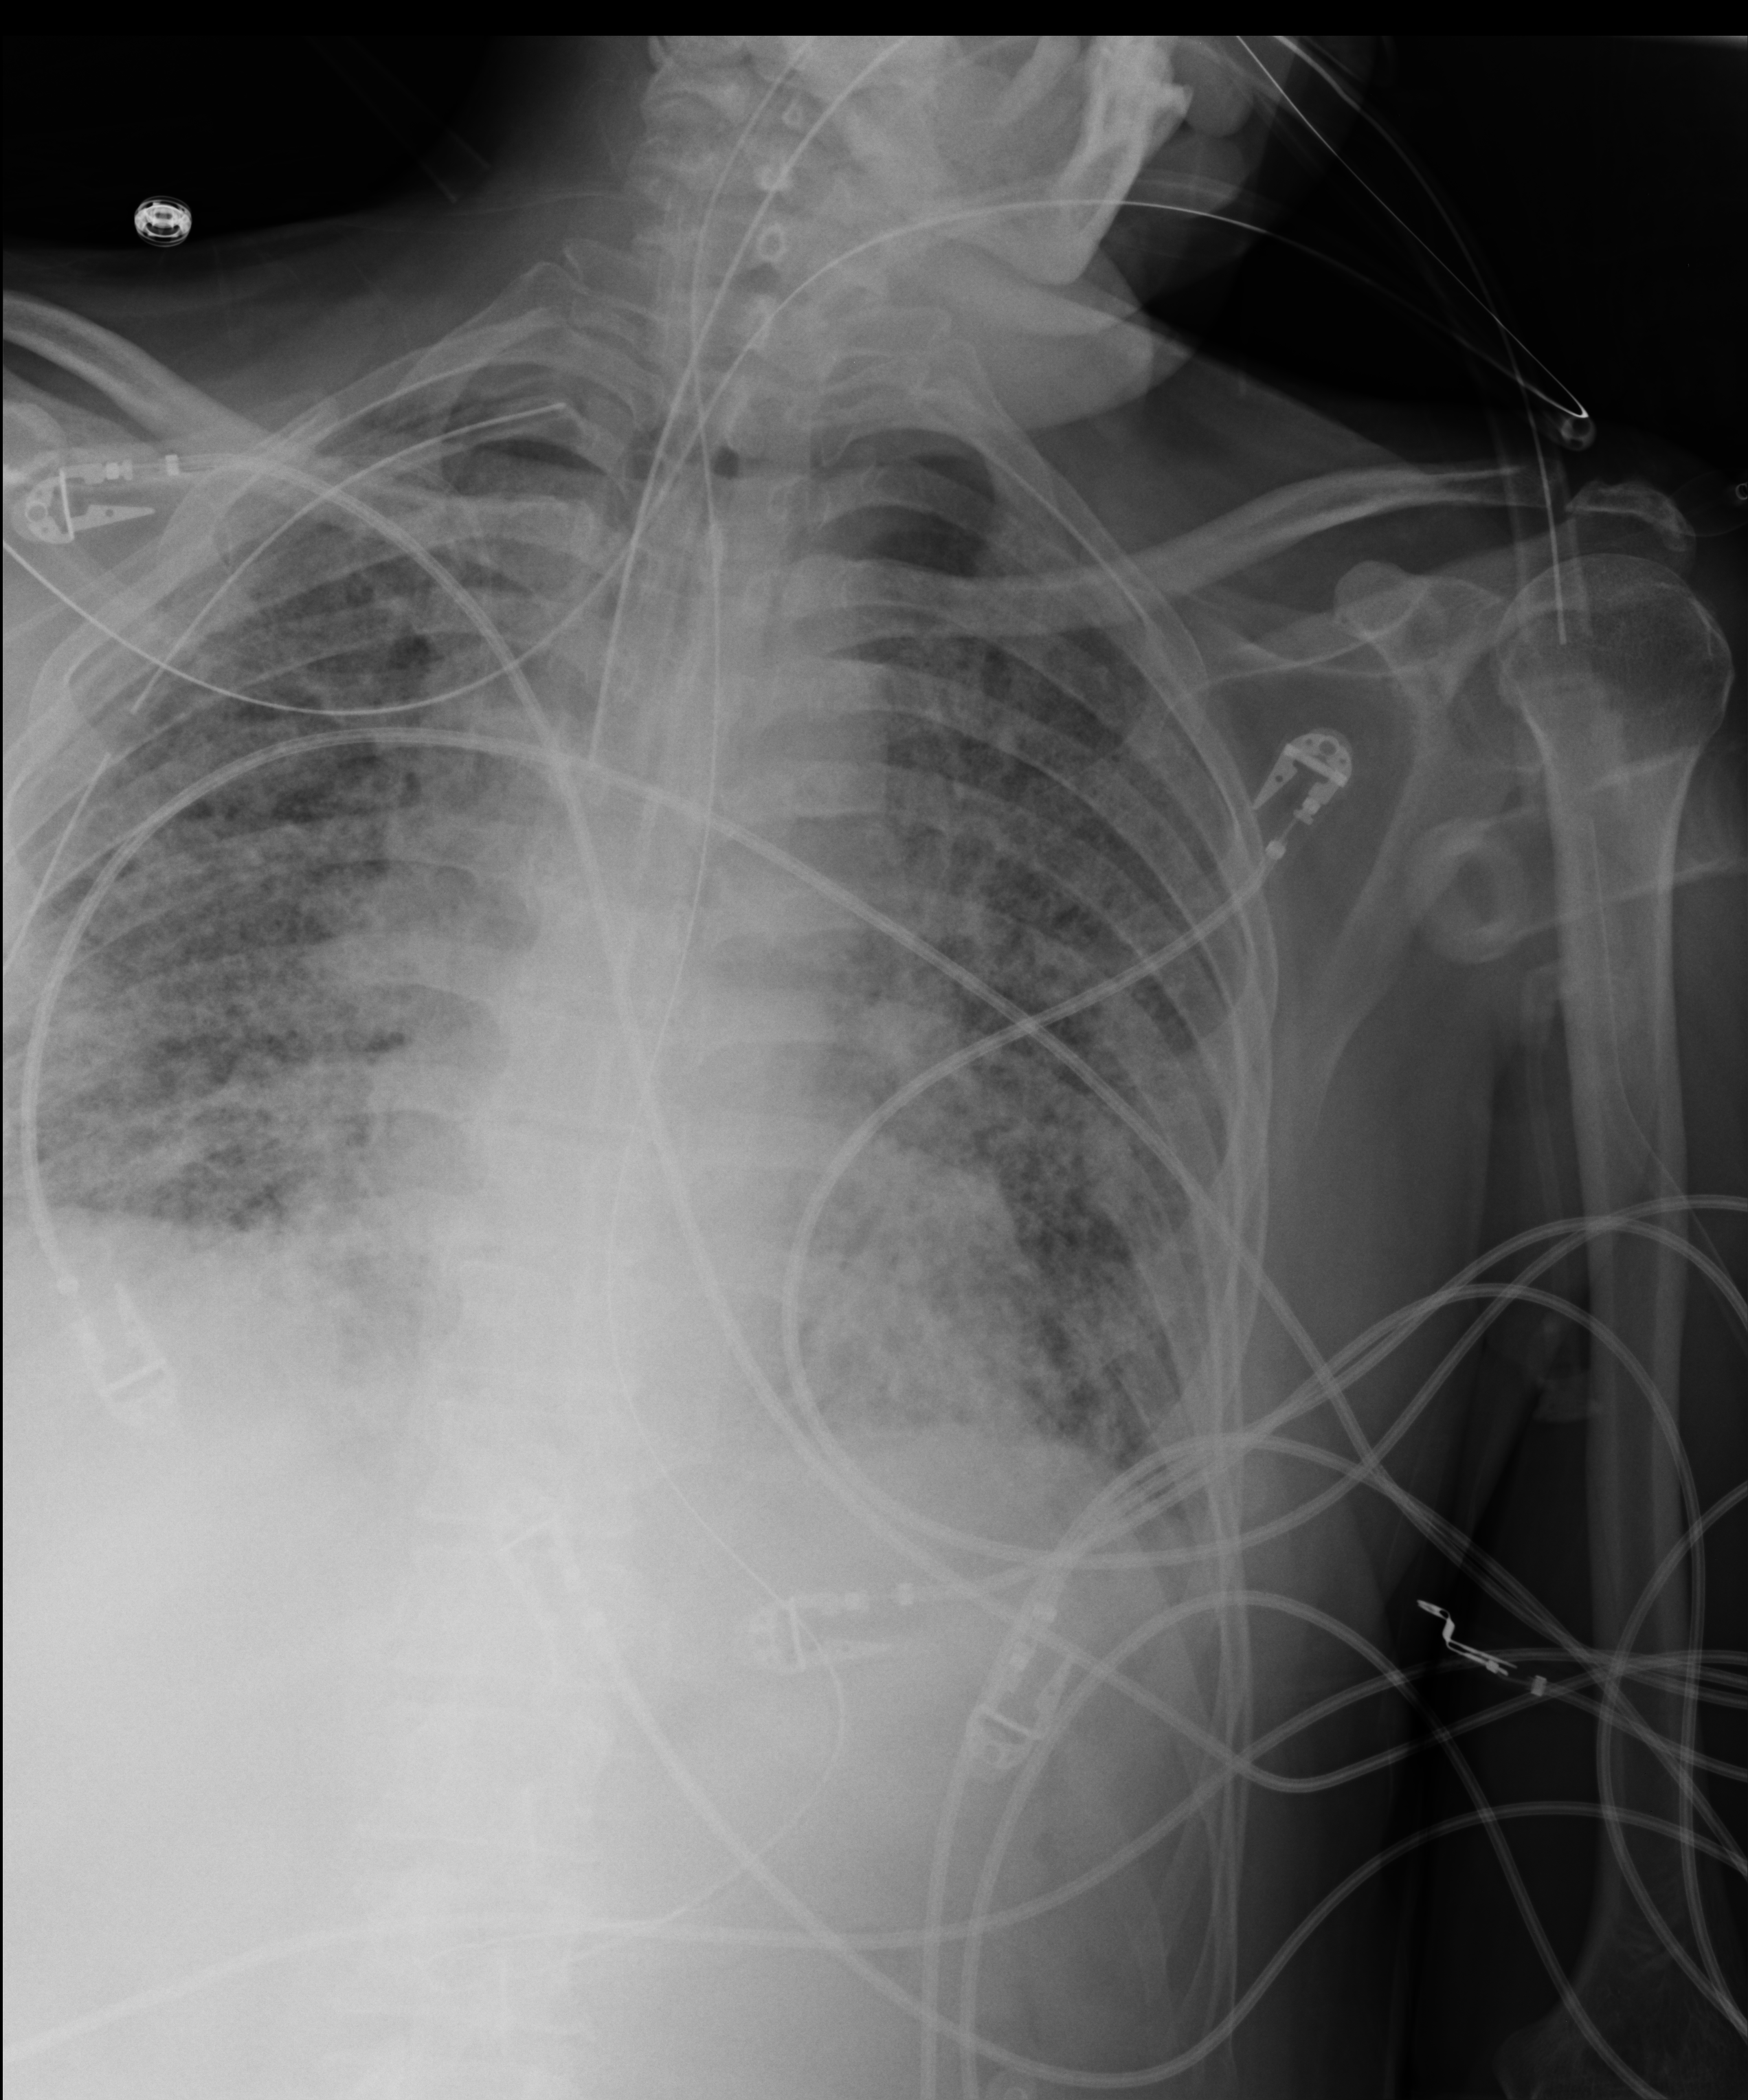
Portable chest radiograph, anteroposterior (AP) projection. Patient hospitalised with COVID-19; male, aged 60–74 years.
From the hospital-stay record, not from the radiograph (when in the stay this image was taken is not recorded):
- COPD (admission record): no